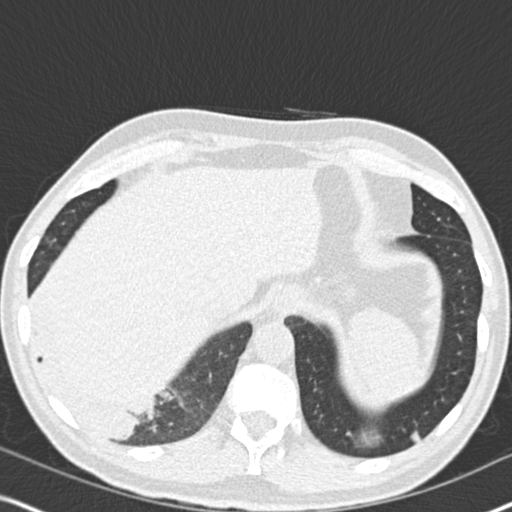
Low-dose screening chest CT, one axial slice; position 48 of 182 along the scan axis; reconstruction kernel B30f; 120 kVp; lung window (W 1500 / L -600 HU); 512 × 512 image matrix, field of view 330 × 330 mm.
Outlined on this slice (expert manual segmentation):
- lesion 1 (tumor, lower lobe of right lung): bounding box <84,395,144,439> (left, top, right, bottom; pixels)